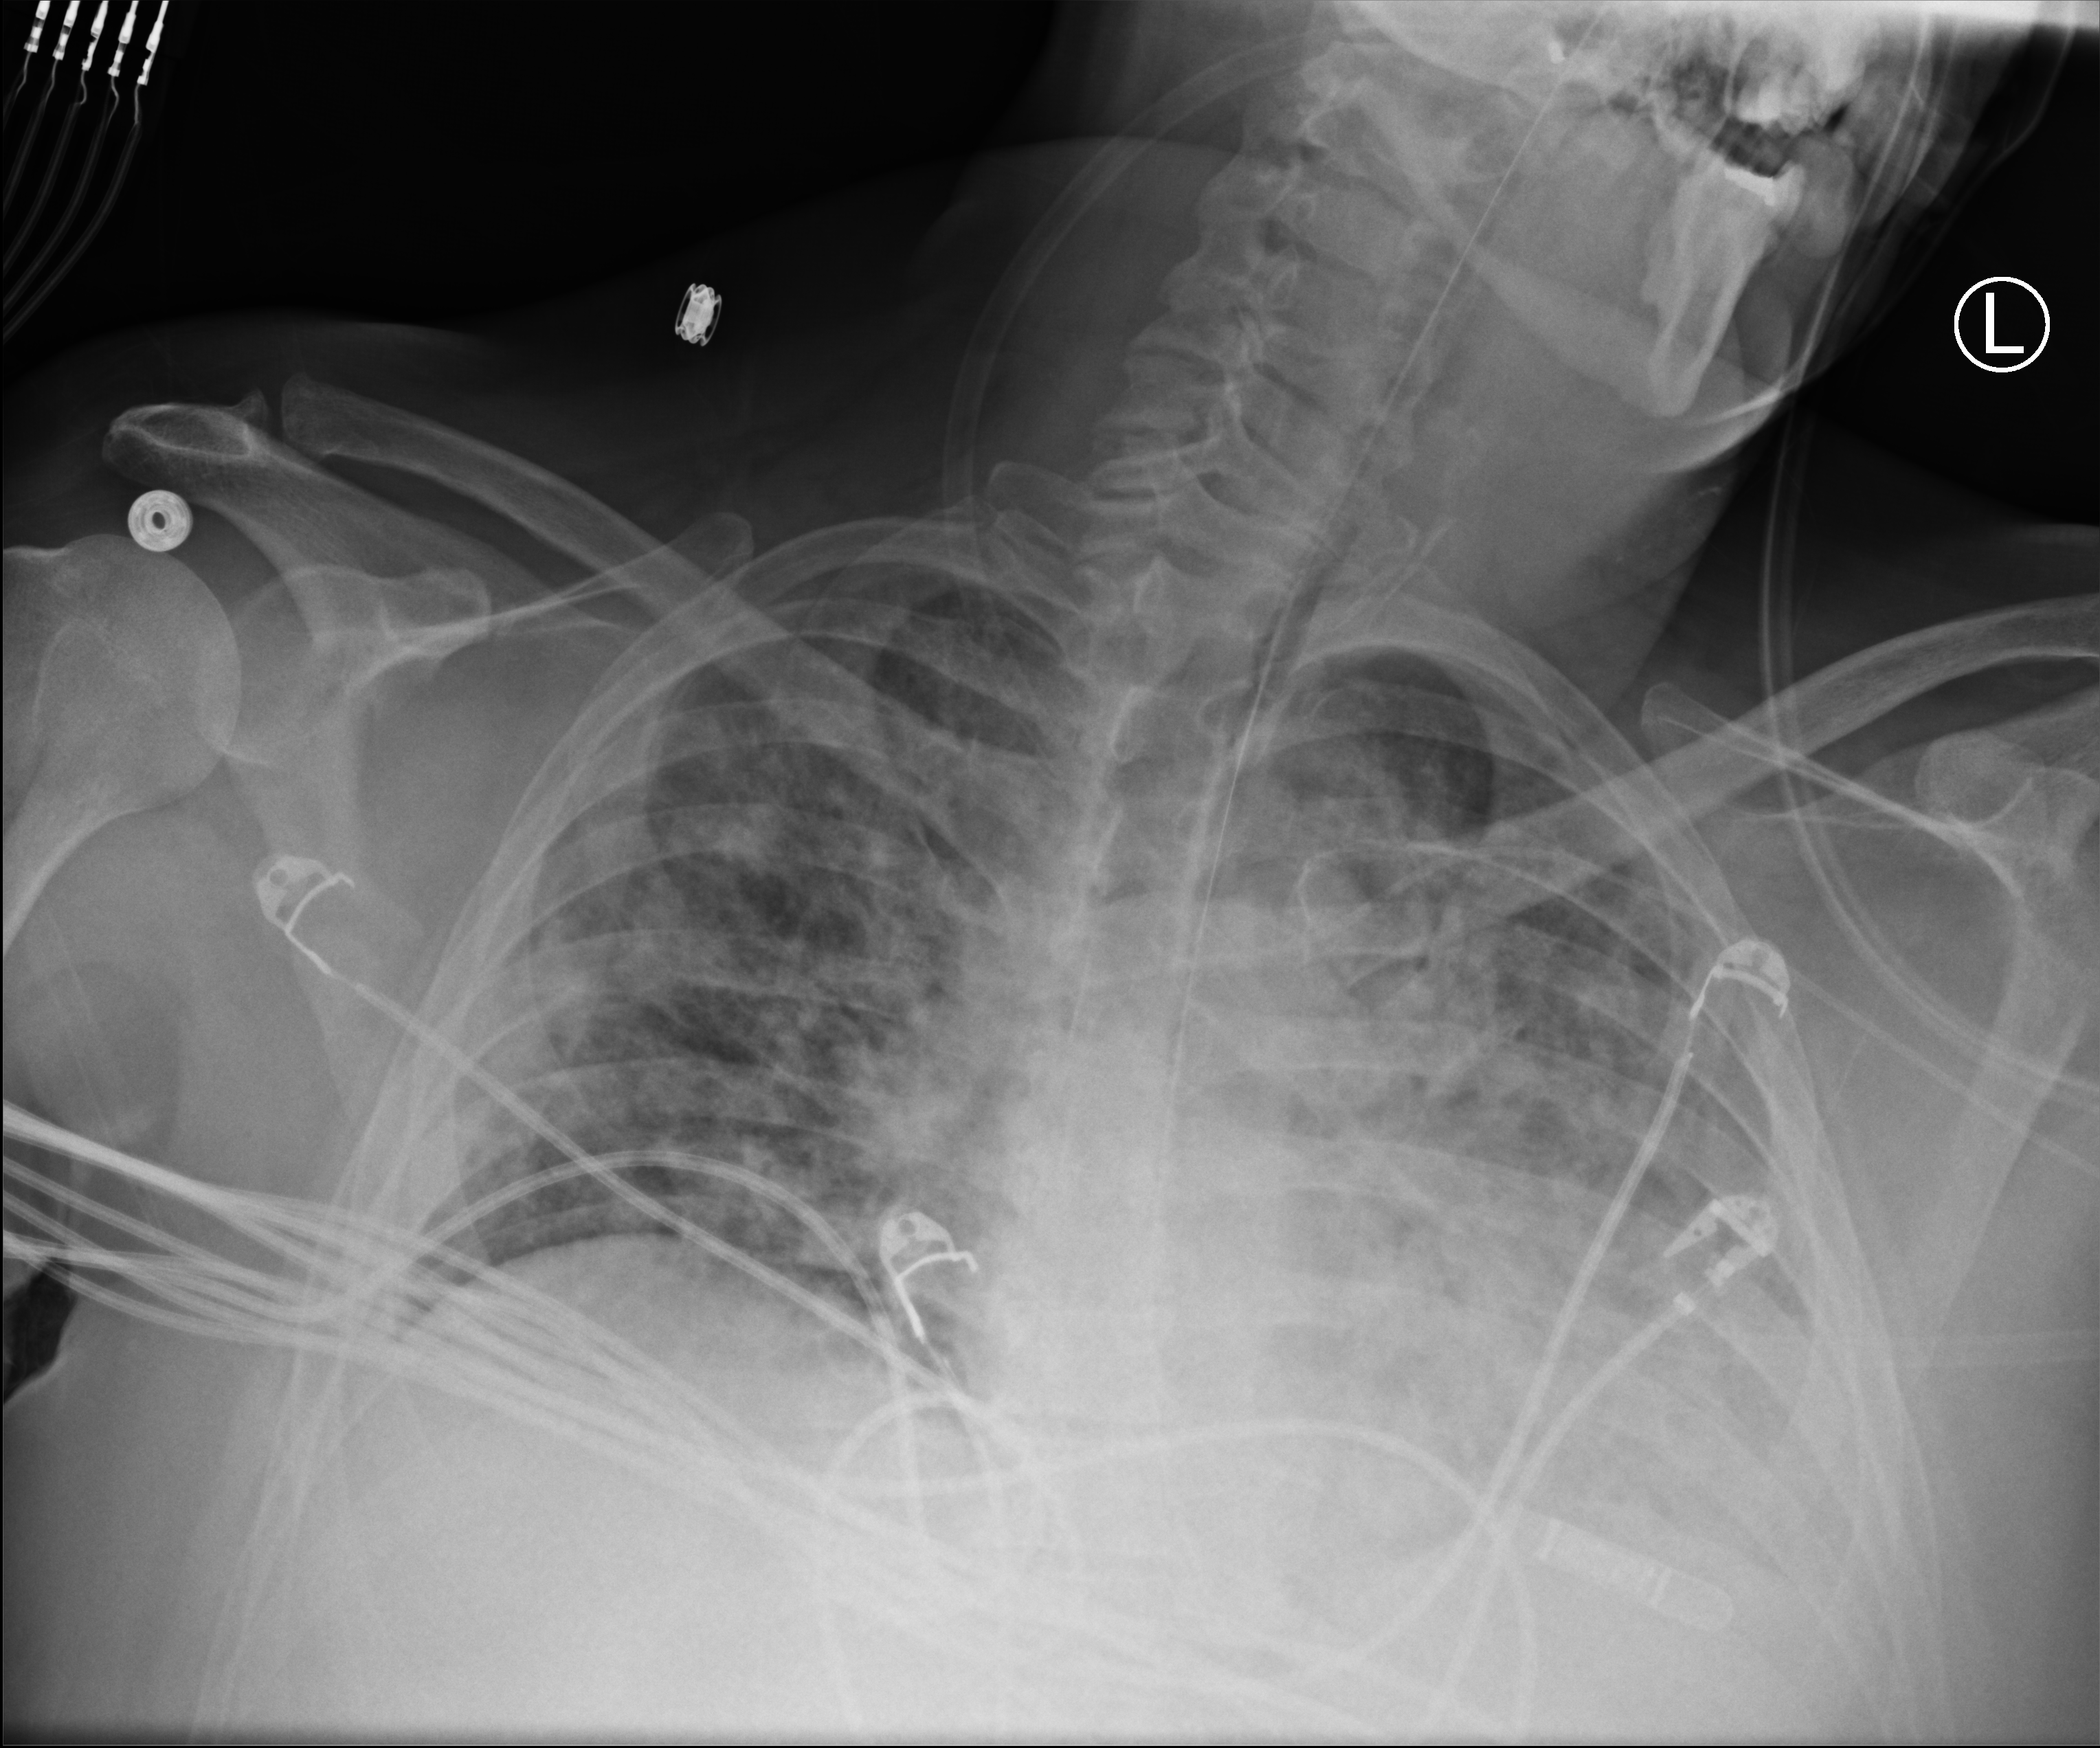
Bedside chest radiograph (computed radiography); anteroposterior (AP) projection. Patient hospitalised with COVID-19; male, aged 18–59 years.
Admission-level facts for this patient (not findings on this image; timing relative to this image not recorded): mechanically ventilated during this hospital stay: yes.